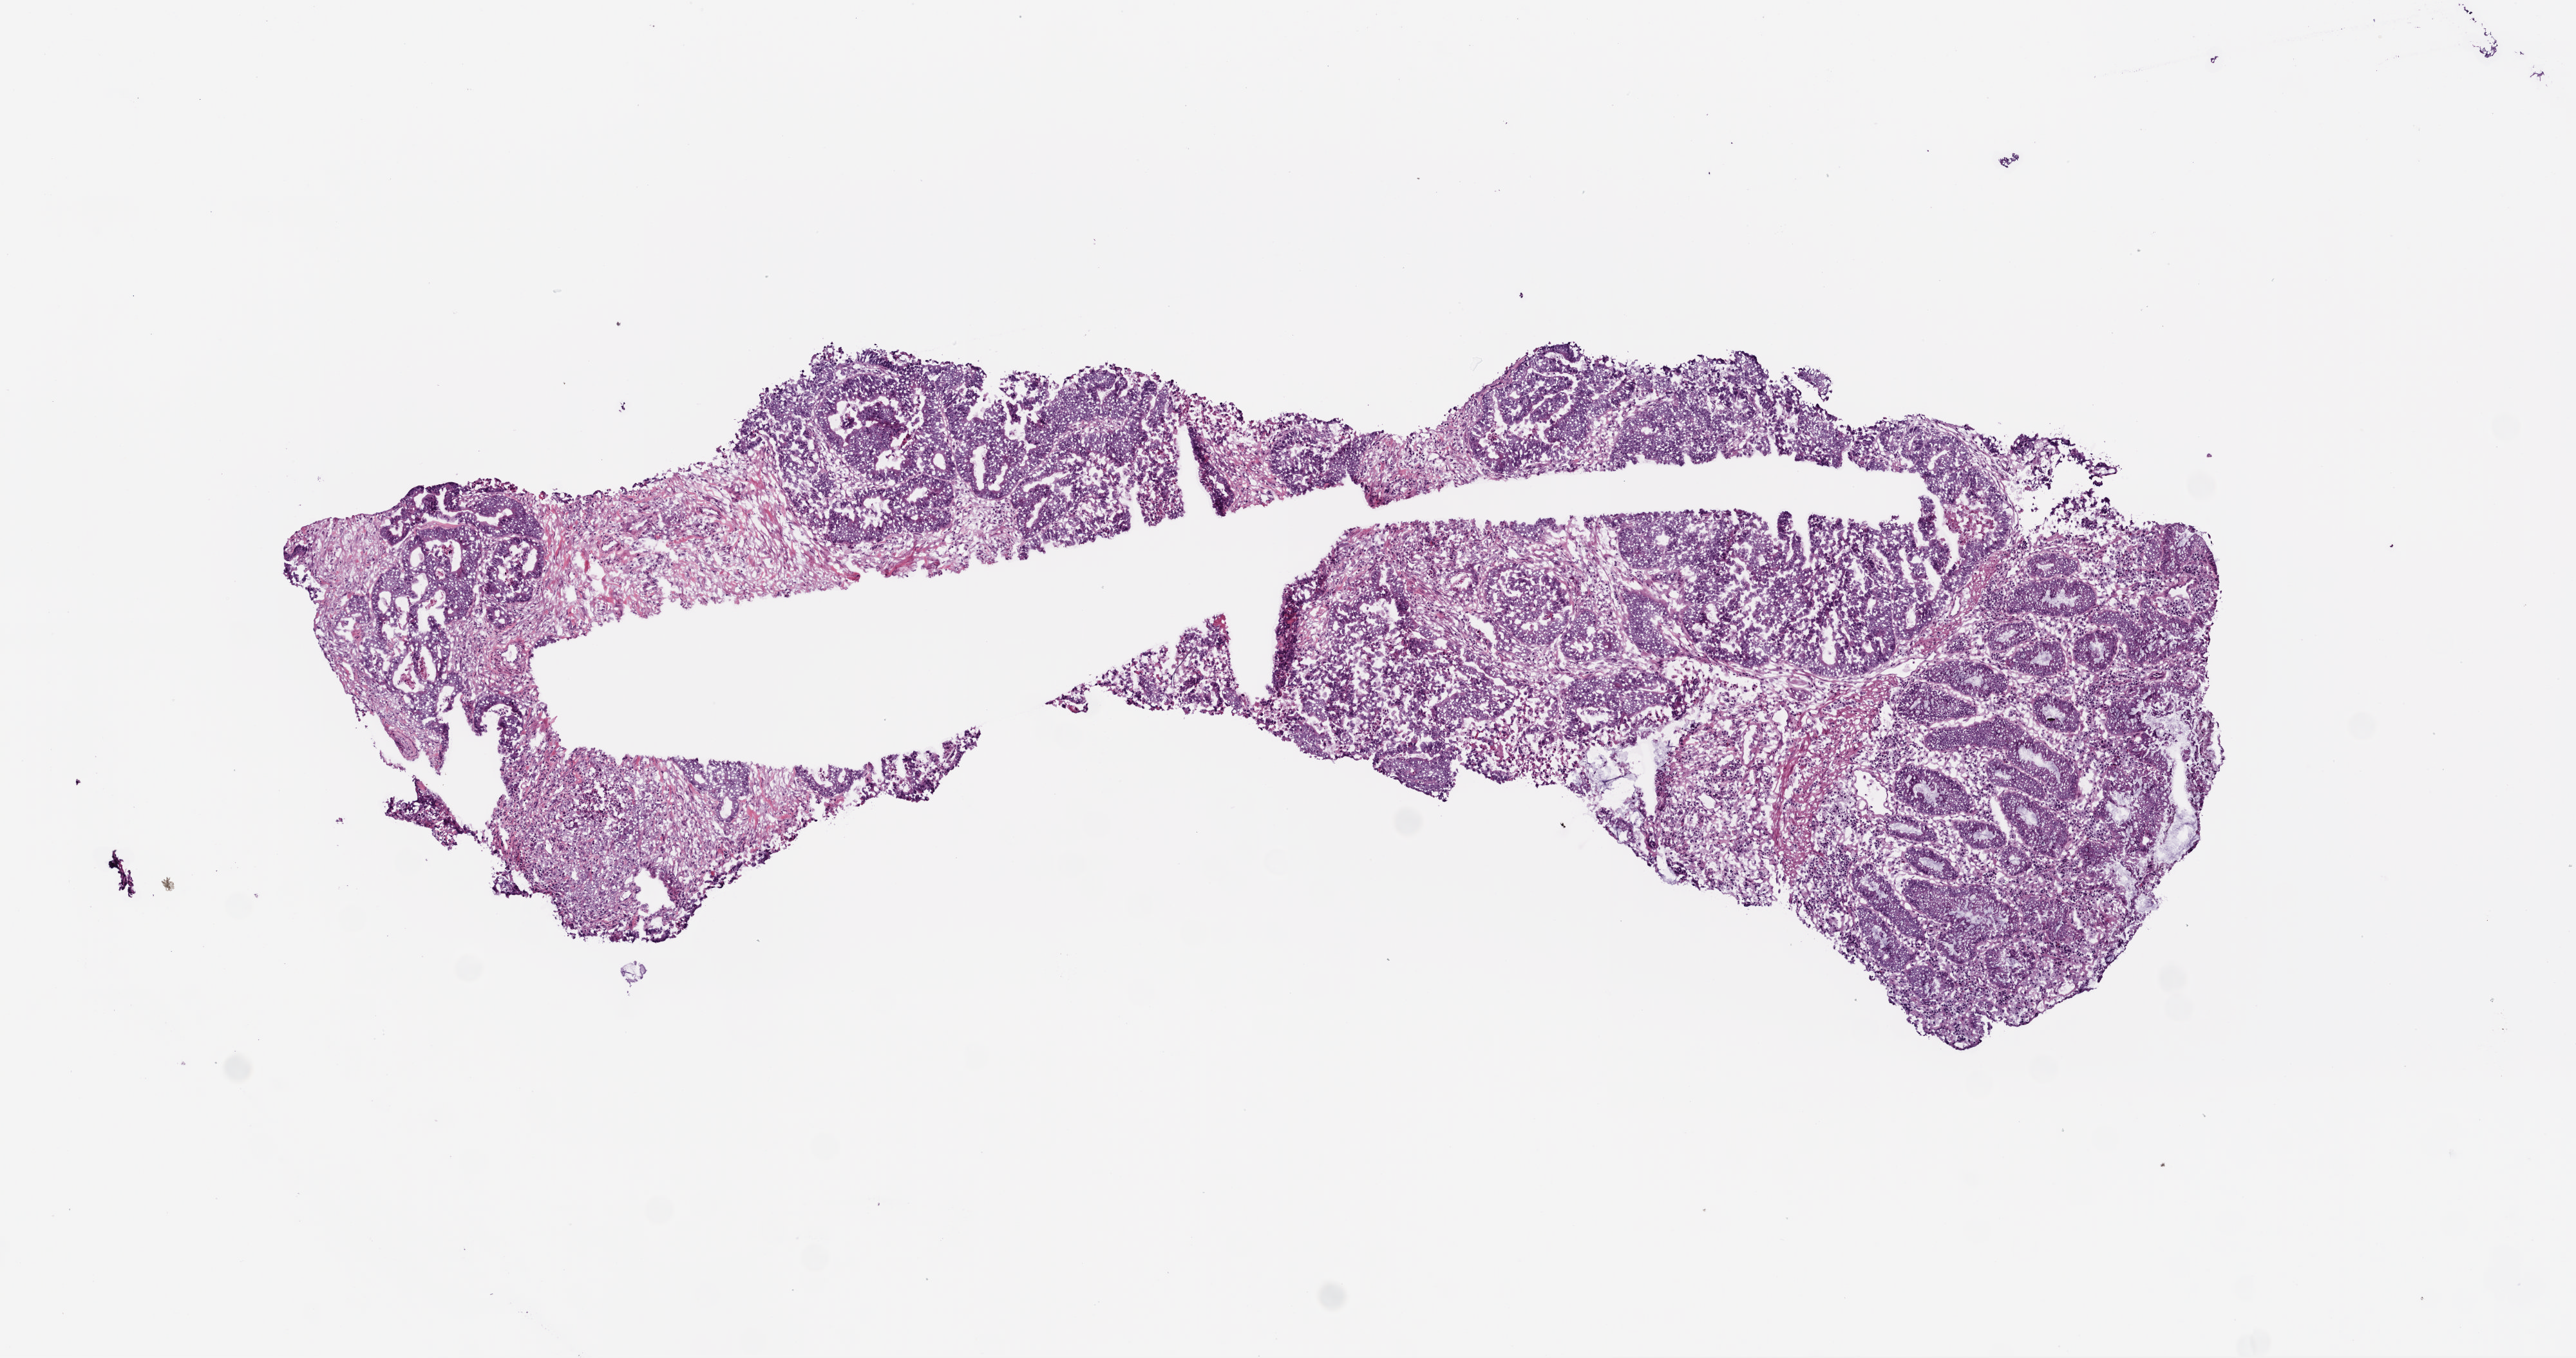
Hematoxylin and eosin (H&E) stained whole-slide image — low-resolution overview of the scanned area, about 8.0 x 4.2 mm. Frozen section from the bottom of the tissue portion. Primary tumour sample from the rectum. Female patient; age at initial diagnosis 79 years. Slide review estimates, as recorded: tumour cells 63%, tumour nuclei 70%, normal cells 20%, stromal cells 15%, necrosis 2%.
Lymph nodes positive (case pathology): 2 of 14 examined. Diagnosis: Adenocarcinoma, NOS.